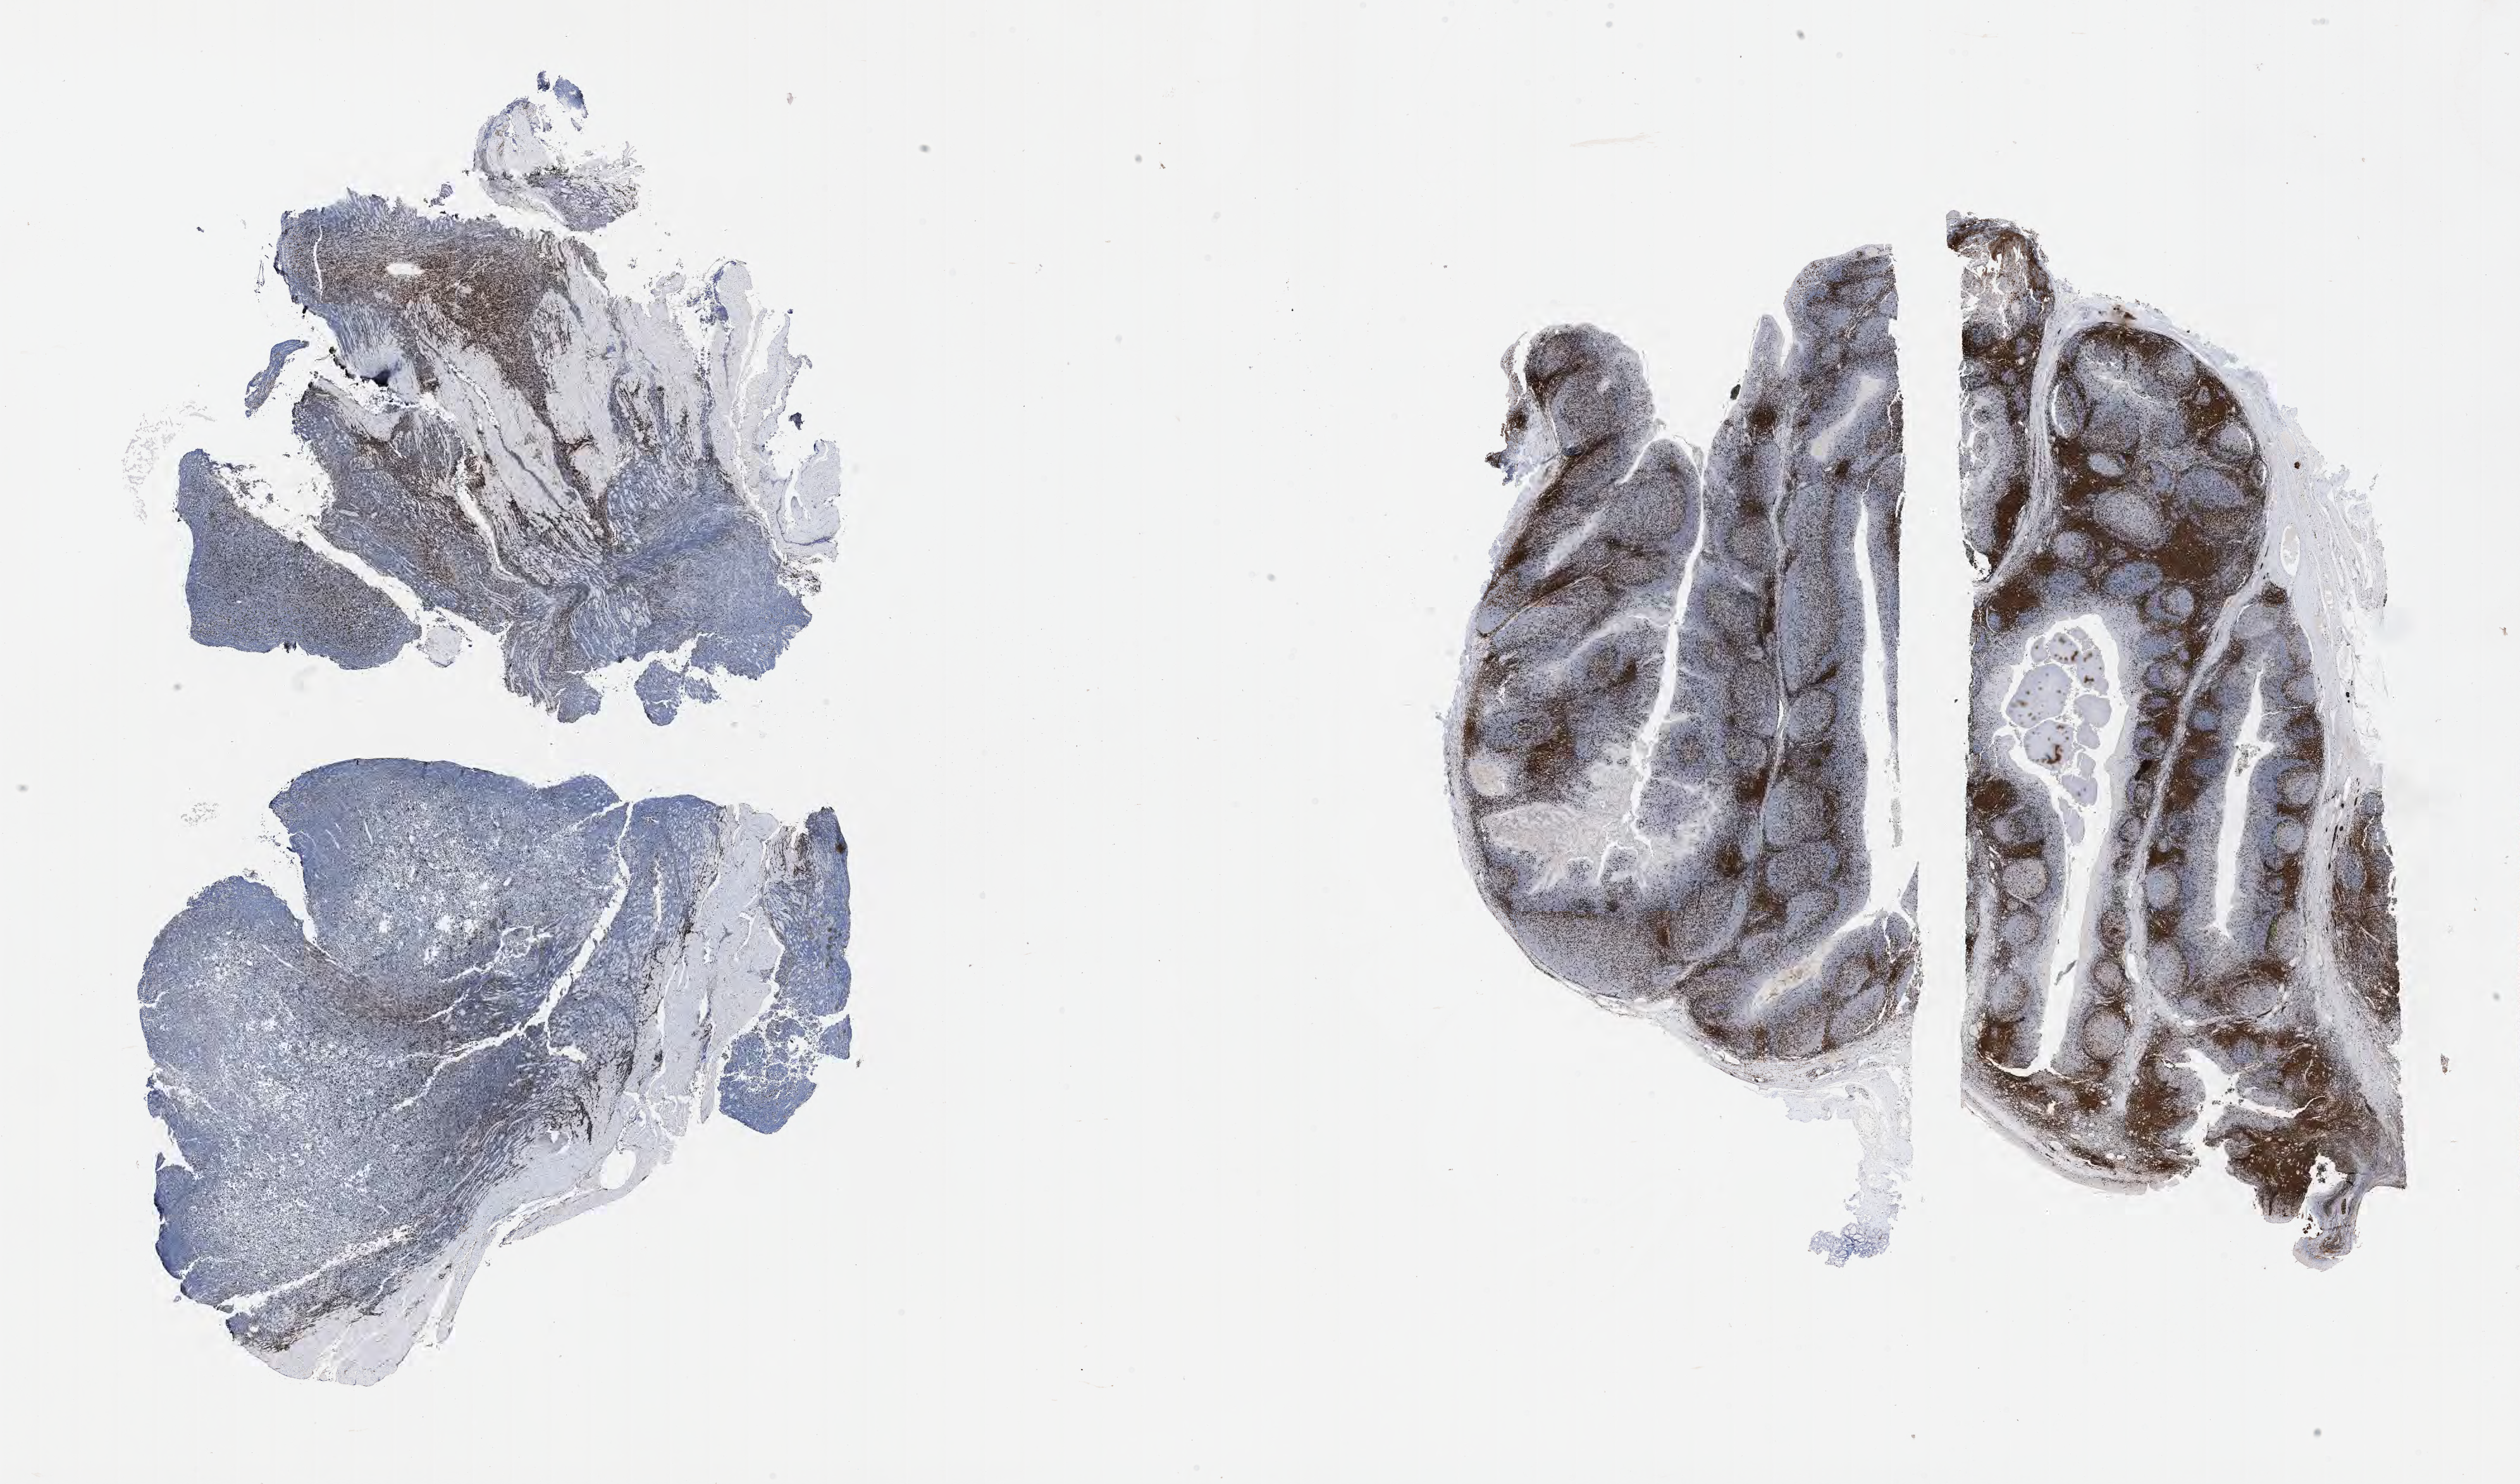
Immunohistochemistry (IHC) whole-slide image stained for CD3 — whole scanned area (about 32.2 x 19.0 mm) shown as a low-resolution overview, specimen: tumor tissue. Patient: male, 40 years old.
Diagnosis: Burkitt lymphoma, NOS.